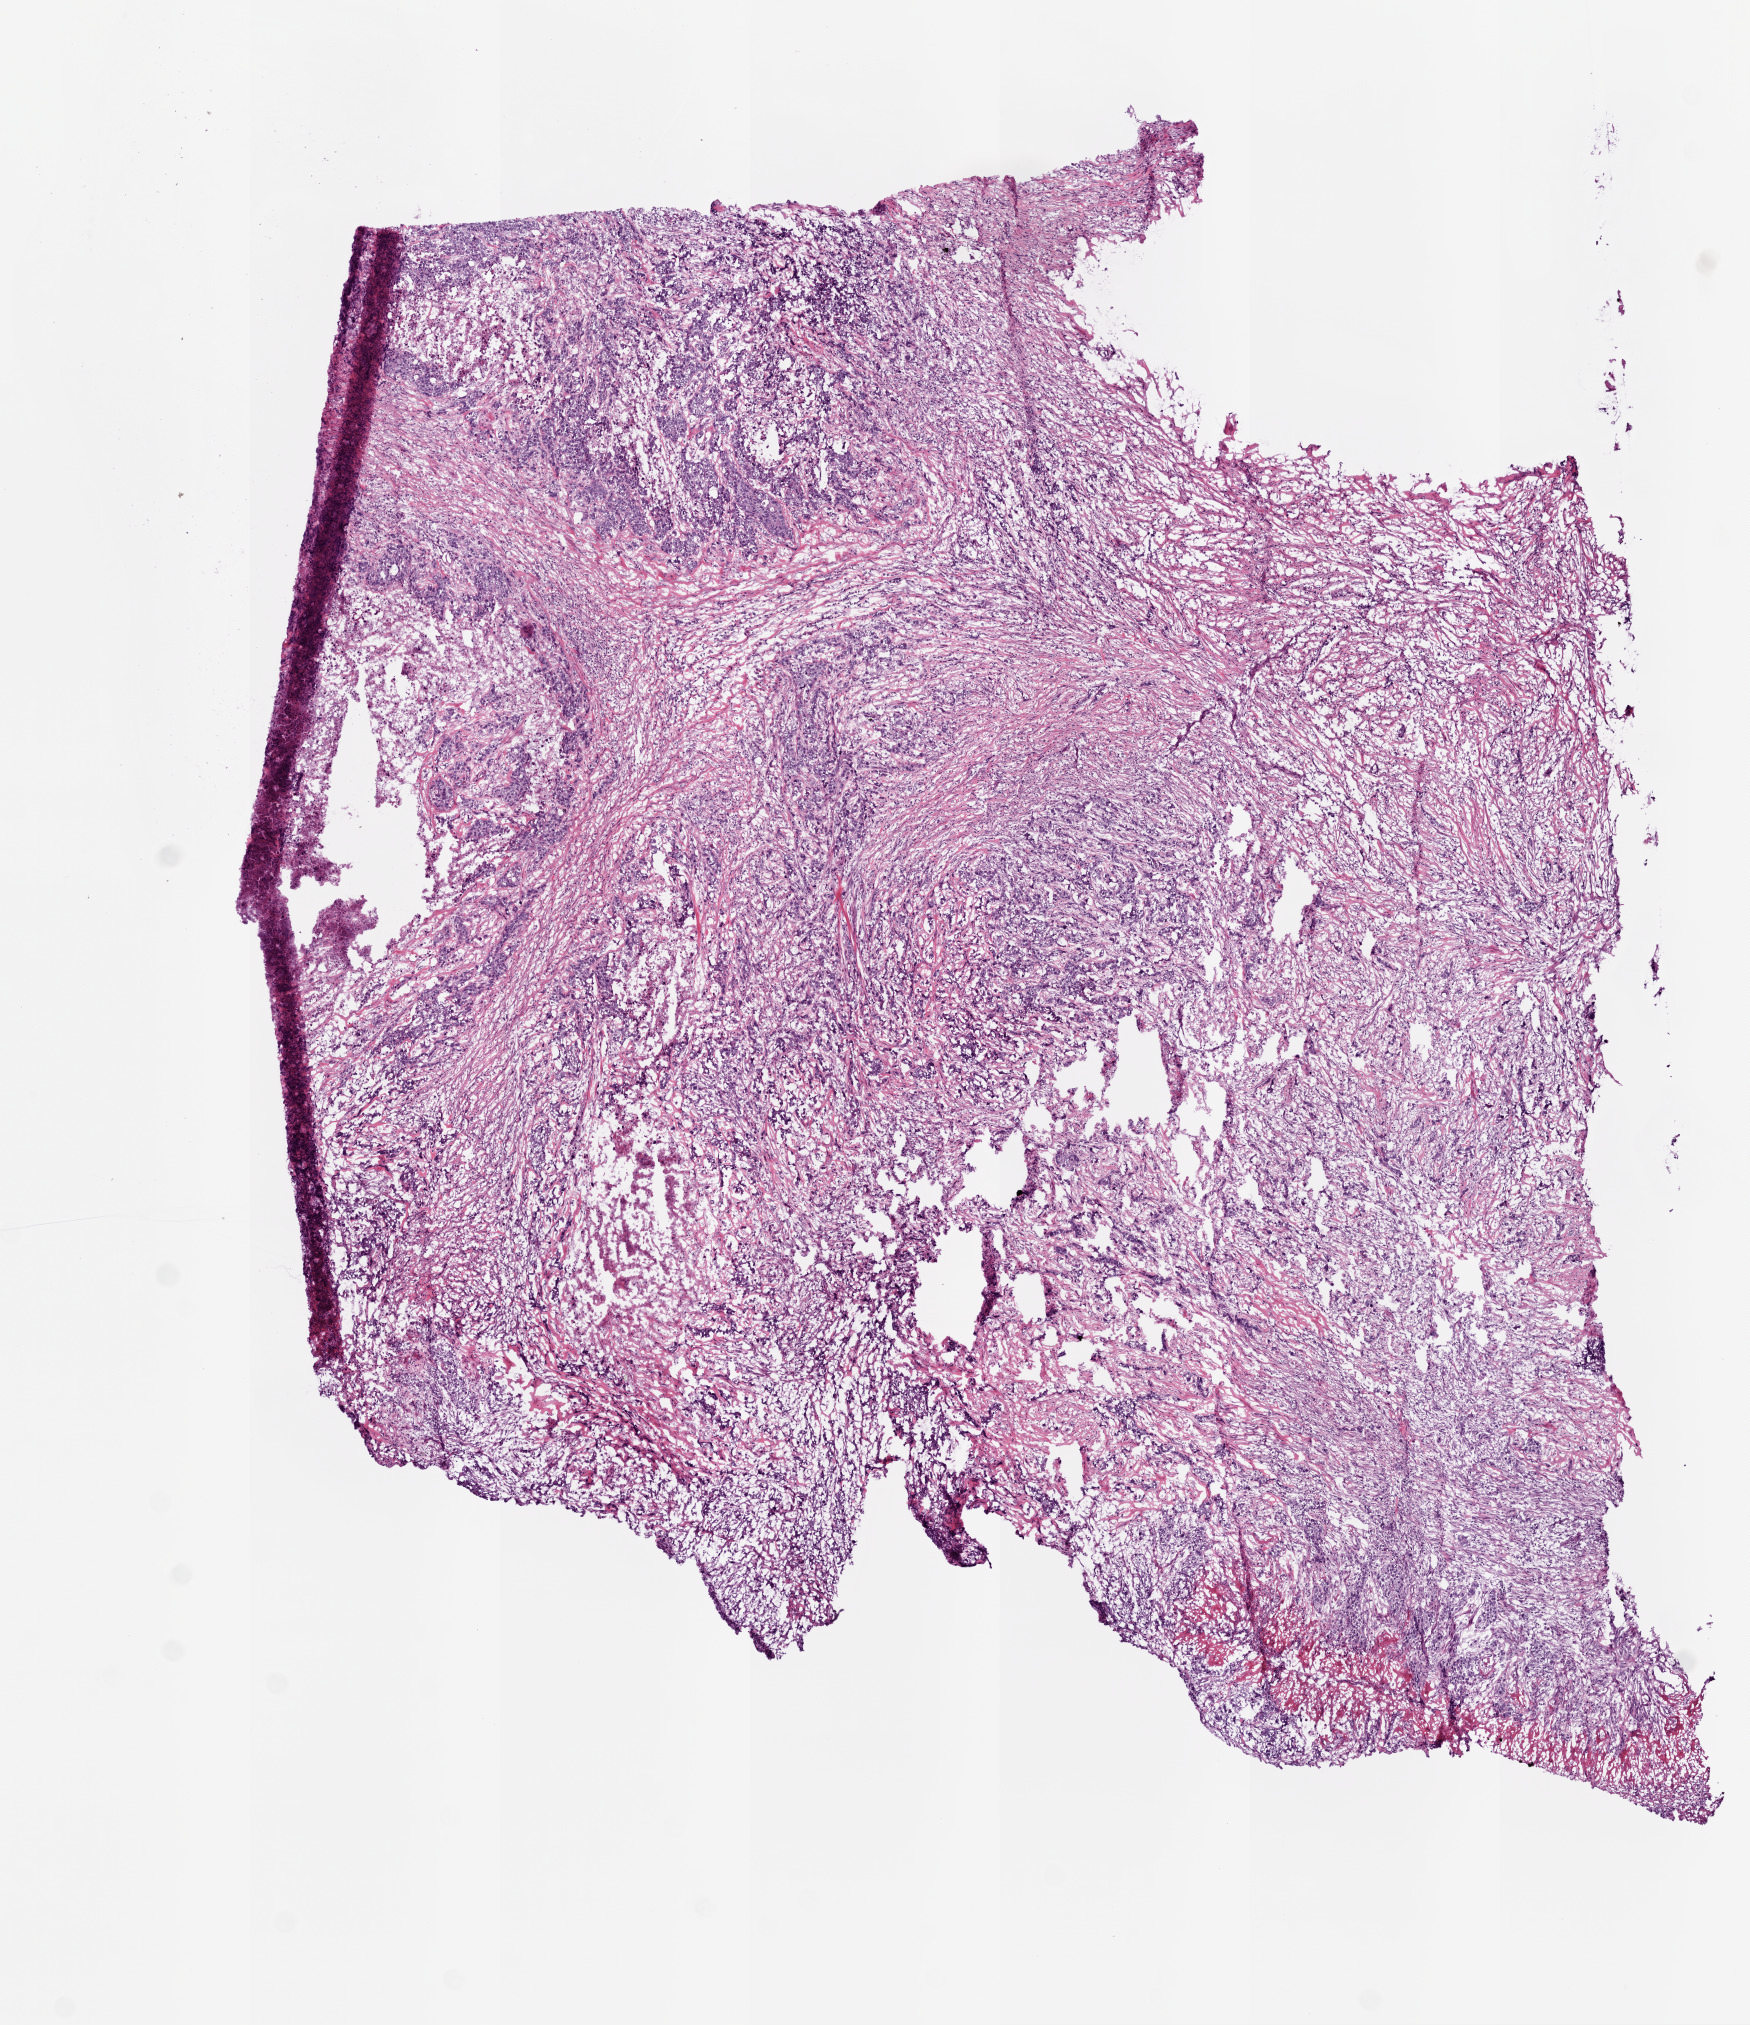
Digitized H&E-stained tissue section (whole slide) — shown as a low-resolution overview of the whole scanned area (about 7.0 x 8.1 mm, from a 20x scan), frozen section from the bottom of the tissue portion, primary tumour sample from the stomach. Male, age 59 years at initial diagnosis. Slide review estimates, as recorded: tumour cells 55%, tumour nuclei 75%.
Diagnosis: Carcinoma, diffuse type.